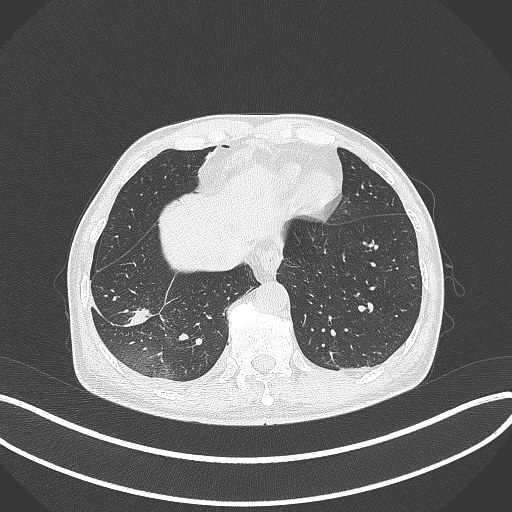
Chest CT, one axial slice. Position 85 of 388 along the scan axis. Reconstruction kernel B70f. 120 kVp. Lung window (W 1500 / L -600 HU). 512 × 512 image matrix, field of view 400 × 400 mm. Male patient, age 64 years. From the clinical record (not read from this slice): clinical TNM (as recorded): T3 N0 M0; histopathological grade: G2-3.
Annotated regions visible in this slice (bounding box drawn by a radiologist):
- lung tumour (recorded histology: adenocarcinoma): bounding box <123,301,155,332> (left, top, right, bottom; pixels)